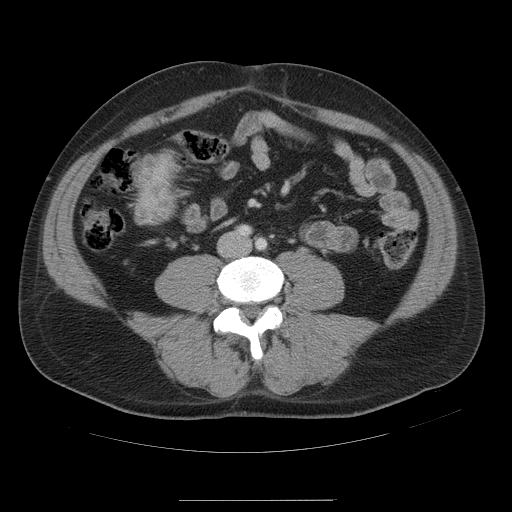
Contrast-enhanced abdominal CT, one axial slice. Slice 4 of 54 in the series (ordered by position). 120 kVp. Intravenous contrast given. Soft-tissue window (W 400 / L 40 HU). 5 mm slice thickness. 512 × 512 image matrix. Male patient, age 40 years. From the clinical record (not read from this slice): diagnosis: colorectal cancer liver metastases, imaged before liver resection; multiple liver metastases: no; largest metastasis: 15 cm.
Outlined on this slice (outlined manually by an expert reader):
- liver: bounding box [x1, y1, x2, y2] px = [134, 153, 175, 224]
- liver metastasis: [139, 156, 170, 221]